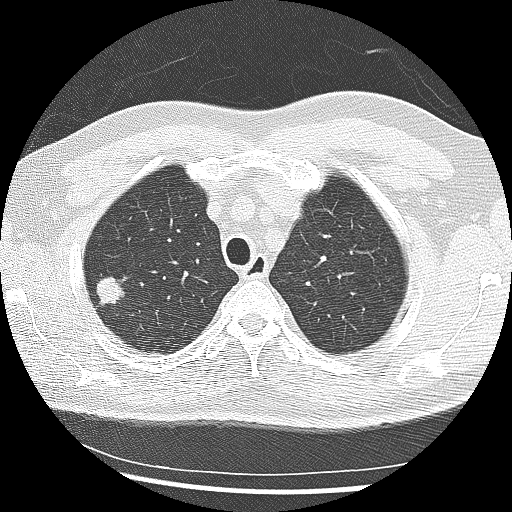
Low-dose screening chest CT, one axial slice; slice 213 of 265 in the series (ordered by position); reconstruction kernel LUNG; 120 kVp; lung window (W 1500 / L -600 HU); 2.5 mm slice thickness; 512 × 512 image matrix, field of view 340 × 340 mm.
Structures marked on this image (outlined manually by an expert reader):
- lesion 1 (tumor, upper lobe of right lung): bounding box (x1, y1, x2, y2) in pixels: (97, 277, 126, 306)